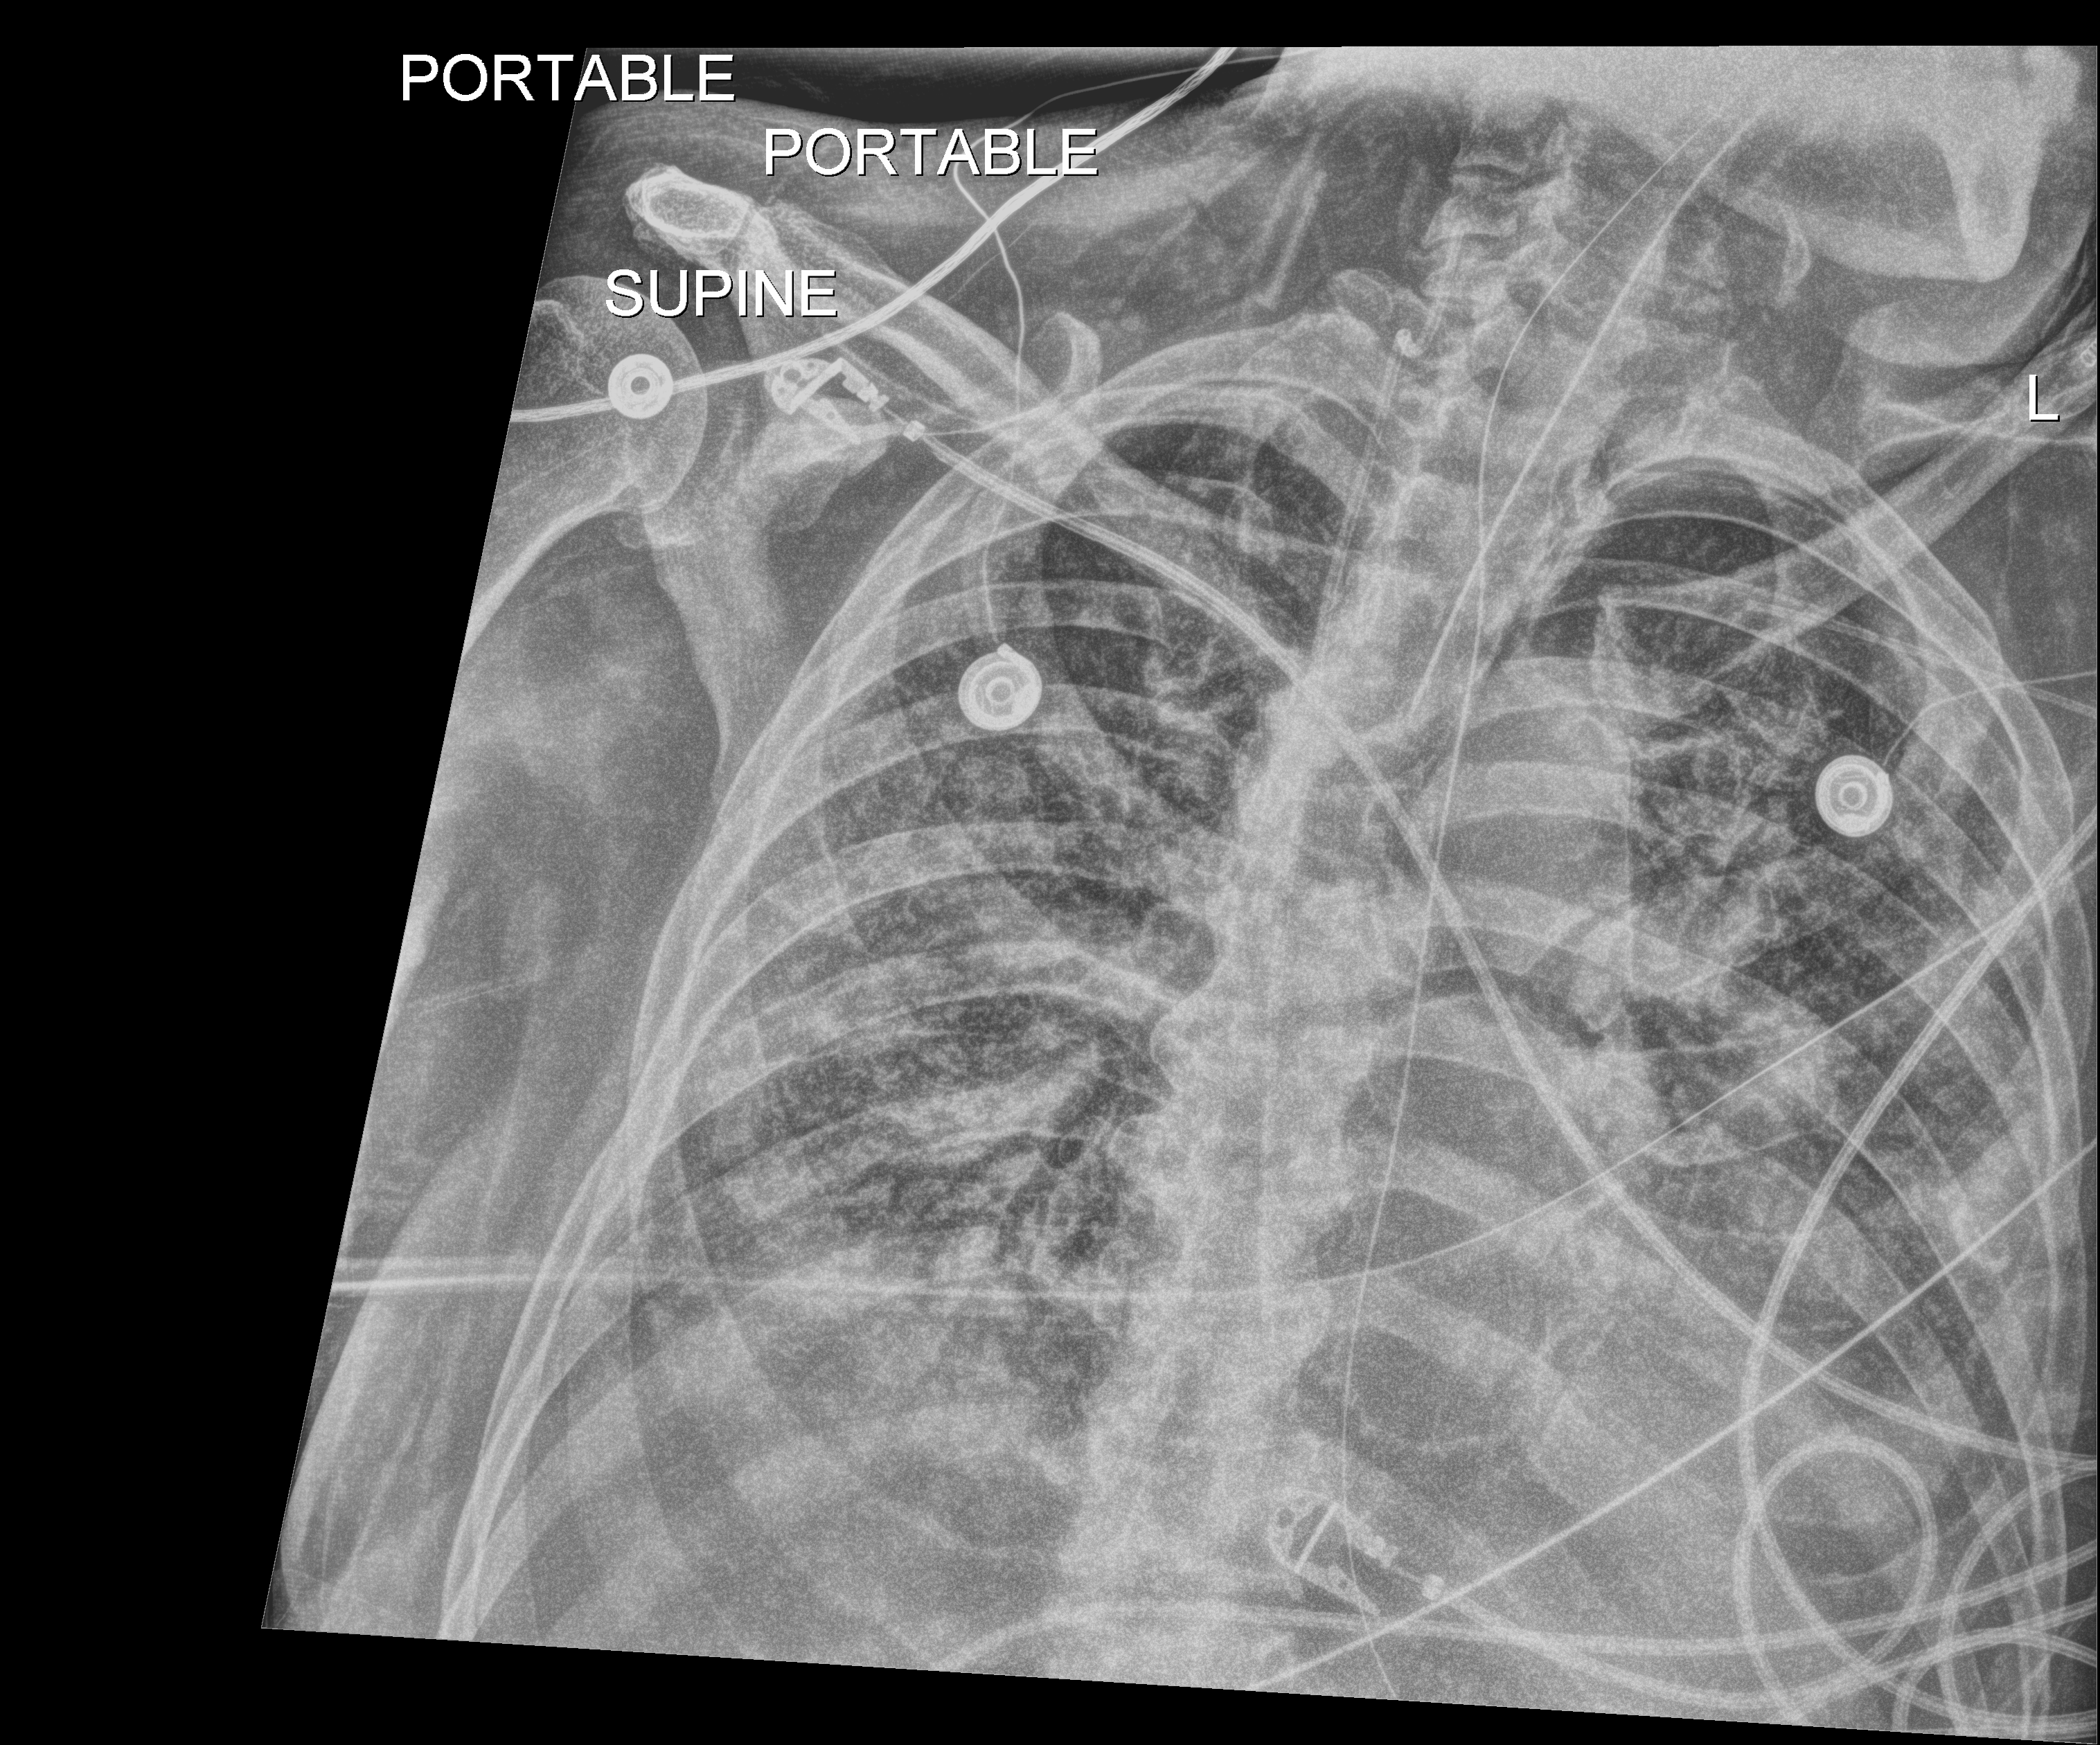
Portable chest radiograph, anteroposterior (AP) projection. Patient hospitalised with COVID-19; male, aged 75–90 years.
Hospital-stay facts (about this admission, not read from this image; timing relative to this image not recorded): admitted to intensive care during this hospital stay: yes; other chronic lung disease (admission record): no; mechanically ventilated during this hospital stay: yes.